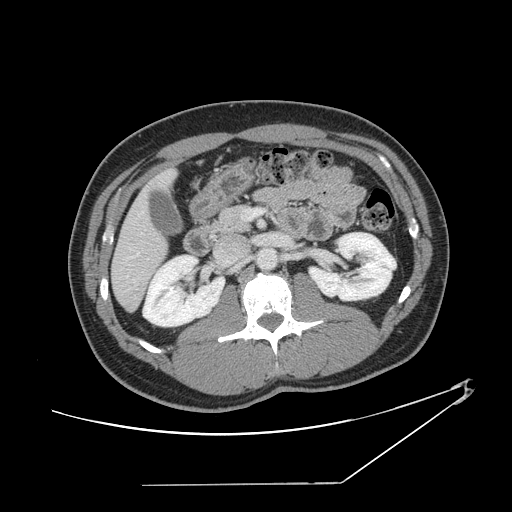
Contrast-enhanced abdominal CT, one axial slice; position 60 of 152 along the scan axis; soft-tissue window (W 400 / L 40 HU); 2.5 mm slice thickness; 512 × 512 image matrix. Male patient, age 45 years. Case-level facts recorded for this patient, not image findings: diagnosis: colorectal cancer liver metastases, imaged before liver resection; multiple liver metastases: no; largest metastasis: 1 cm; disease in both lobes: no.
Structures marked on this image (expert manual segmentation):
- hepatic veins: bounding box <125,251,140,260> (left, top, right, bottom; pixels)
- liver: <113,173,173,310>
- planned liver remnant (the part of the liver to remain after resection): <113,173,173,310>
- portal vein (with intrahepatic branches): <246,209,263,220>